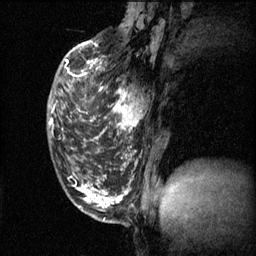
Breast MRI (dynamic contrast-enhanced), one sagittal slice. Slice 20 of 60 in the series (ordered by position). 3 images stored at this slice position (order not interpretable as contrast timing). 1.5 T. TE 4.2 ms, TR 11.1 ms. 2 mm slice thickness. 256 × 256 image matrix, field of view 180 × 180 mm. Patient: female, 50 years.
Annotated regions visible in this slice (semi-automatic segmentation, software-assisted and operator-edited):
- analysis volume of interest (the breast-tissue region the enhancement analysis was run in; not a lesion): box from (x=73, y=68) to (x=146, y=141) px
- tumour enhancement mask (voxels above the 70 % enhancement threshold inside the analysis volume of interest): (x=73, y=68)–(x=142, y=141)